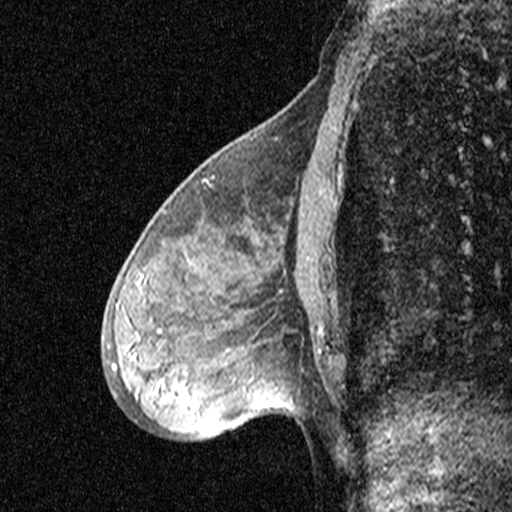
Breast MRI (dynamic contrast-enhanced), one sagittal slice; position 18 of 44 along the scan axis; dynamic contrast-enhanced study with each time point stored as its own series, time point 2 of 3 at this slice position (early post-contrast, ordered by acquisition time); 1.5 T; TE 4.5 ms, TR 11 ms; 3 mm slice thickness; 512 × 512 image matrix, field of view 200 × 200 mm. Patient: female, 53 years. Case-level facts recorded for this patient, not image findings: setting: breast cancer imaged before/during neoadjuvant chemotherapy; receptor status: HR-positive, HER2-negative.
Outlined on this slice (semi-automatic segmentation, software-assisted and operator-edited):
- analysis volume of interest (the breast-tissue region the enhancement analysis was run in; not a lesion): bounding box [x1, y1, x2, y2] px = [88, 176, 313, 423]
- tumour enhancement mask (voxels above the 90 % enhancement threshold inside the analysis volume of interest): [168, 385, 189, 402]